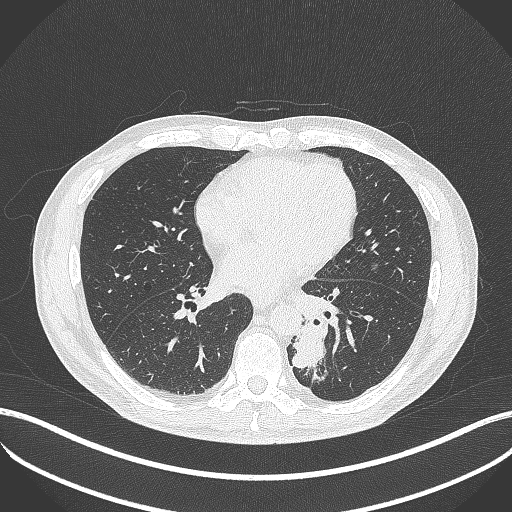
Chest CT, one axial slice. Position 173 of 451 along the scan axis. Reconstruction kernel B70f. 120 kVp. Lung window (W 1500 / L -600 HU). 1 mm slice thickness. 512 × 512 image matrix. Male patient, age 72 years. Case-level facts recorded for this patient, not image findings: clinical TNM (as recorded): T2b N0 M1.
Structures marked on this image (bounding box drawn by a radiologist):
- lung tumour (recorded histology: adenocarcinoma): bounding box (x1, y1, x2, y2) in pixels: (289, 315, 329, 373)